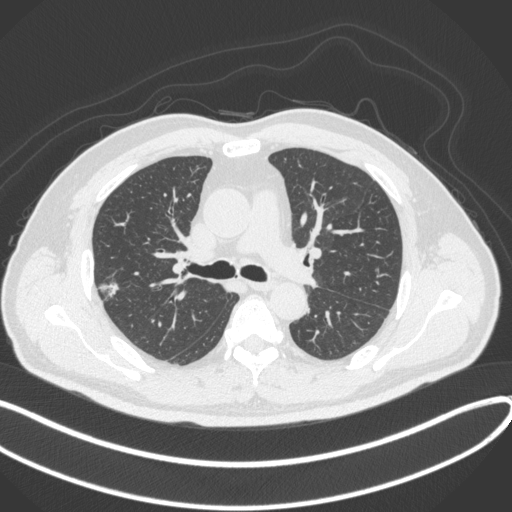
Chest CT, one axial slice. Position 216 of 373 along the scan axis. 120 kVp. Lung window (W 1500 / L -600 HU). 1 mm slice thickness. 512 × 512 image matrix, field of view 400 × 400 mm. Patient: male, 60 years. From the clinical record (not read from this slice): clinical TNM (as recorded): T1c N0 M0.
Outlined on this slice (rectangle marked by the reading radiologist):
- lung tumour (recorded histology: adenocarcinoma): bounding box (x1, y1, x2, y2) in pixels: (94, 274, 126, 307)